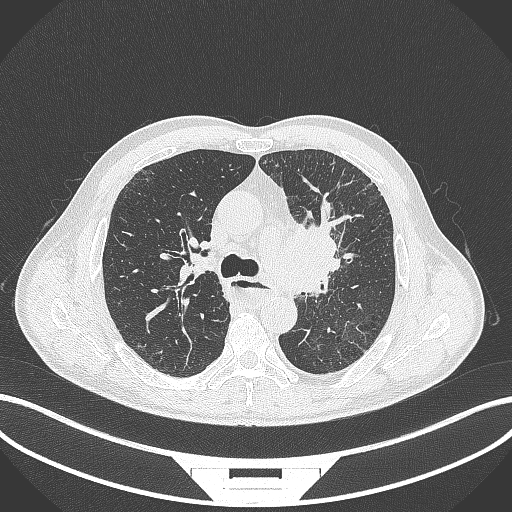
Chest CT, one axial slice; slice 252 of 411 in the series (ordered by position); 120 kVp; lung window (W 1500 / L -600 HU); 512 × 512 image matrix. Male patient, age 57 years. From the clinical record (not read from this slice): clinical TNM (as recorded): T2a N1 M0.
Outlined on this slice (rectangle marked by the reading radiologist):
- lung tumour (recorded histology: squamous cell carcinoma): box from (x=273, y=209) to (x=351, y=302) px